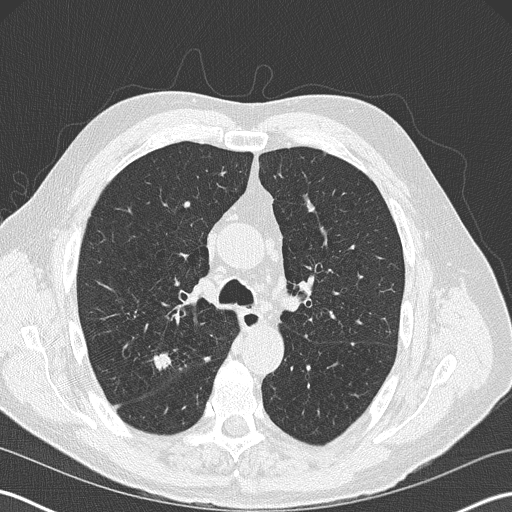
Low-dose screening chest CT, one axial slice; position 127 of 199 along the scan axis; reconstruction kernel B50f; lung window (W 1500 / L -600 HU); 2 mm slice thickness; 512 × 512 image matrix, field of view 350 × 350 mm.
Structures marked on this image (manually delineated by an expert):
- lesion 1 (tumor, upper lobe of right lung): box from (x=155, y=351) to (x=173, y=373) px